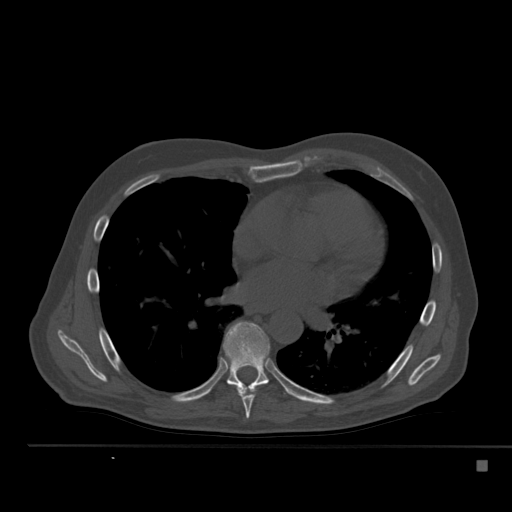
CT including the spine, one axial slice. Reconstruction kernel Br40s. 120 kVp. Bone window (W 1800 / L 400 HU). 1.5 mm slice thickness. 512 × 512 image matrix, field of view 408 × 408 mm. Patient: male, 70 years. Case-level facts recorded for this patient, not image findings: primary cancer: renal.
Annotated regions visible in this slice (semi-automatic segmentation, software-assisted and operator-edited):
- T7 vertebra: bounding box [x1, y1, x2, y2] px = [230, 364, 261, 419]
- T8 vertebra: [223, 322, 288, 394]